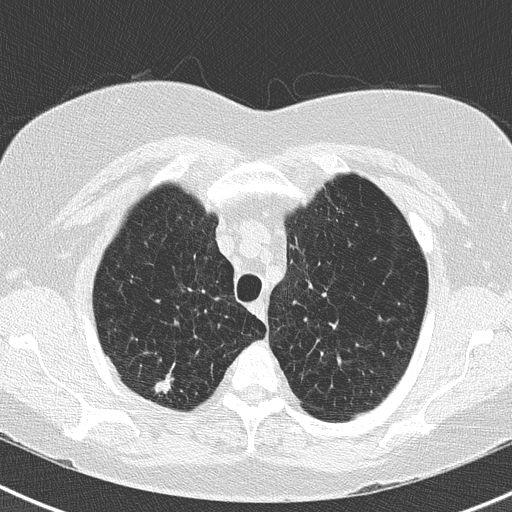
Axial slice from a low-dose chest CT screening exam, second annual screen, lung window (W 1500 / L -600 HU), 2 mm slice thickness, slice 40 of 183 in the series. Female, age 73 years at enrolment. Former smoker at enrolment.
• Lesion marked by an expert reader, bounding box [x1, y1, x2, y2] px = [139, 360, 191, 402].
• The screening reader recorded 2 non-calcified nodules or masses ≥4 mm on this exam (right upper lobe, right upper lobe); which of them this box marks is not recorded.
• Official screen result: positive, no significant change: stable abnormalities potentially related to lung cancer, unchanged since the prior screening exam.
• Later outcome: lung cancer diagnosed 250 days after this screen — adenocarcinoma, NOS, right upper lobe, moderately differentiated (G2), stage IB (AJCC 6th edition), 15 mm at pathology.